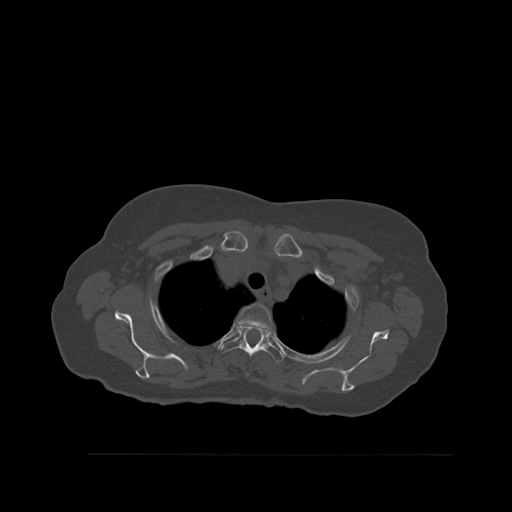
CT including the spine, one axial slice; position 424 of 527 along the scan axis; bone window (W 1800 / L 400 HU); 1.5 mm slice thickness; 512 × 512 image matrix, field of view 470 × 470 mm. Patient: female, 73 years. Case-level facts recorded for this patient, not image findings: primary cancer: breast; vertebrae with lytic lesions (as recorded): L2.
Outlined on this slice (semi-automatically segmented with operator editing):
- T2 vertebra: box from (x=238, y=304) to (x=273, y=330) px
- T3 vertebra: (x=220, y=322)–(x=284, y=362)